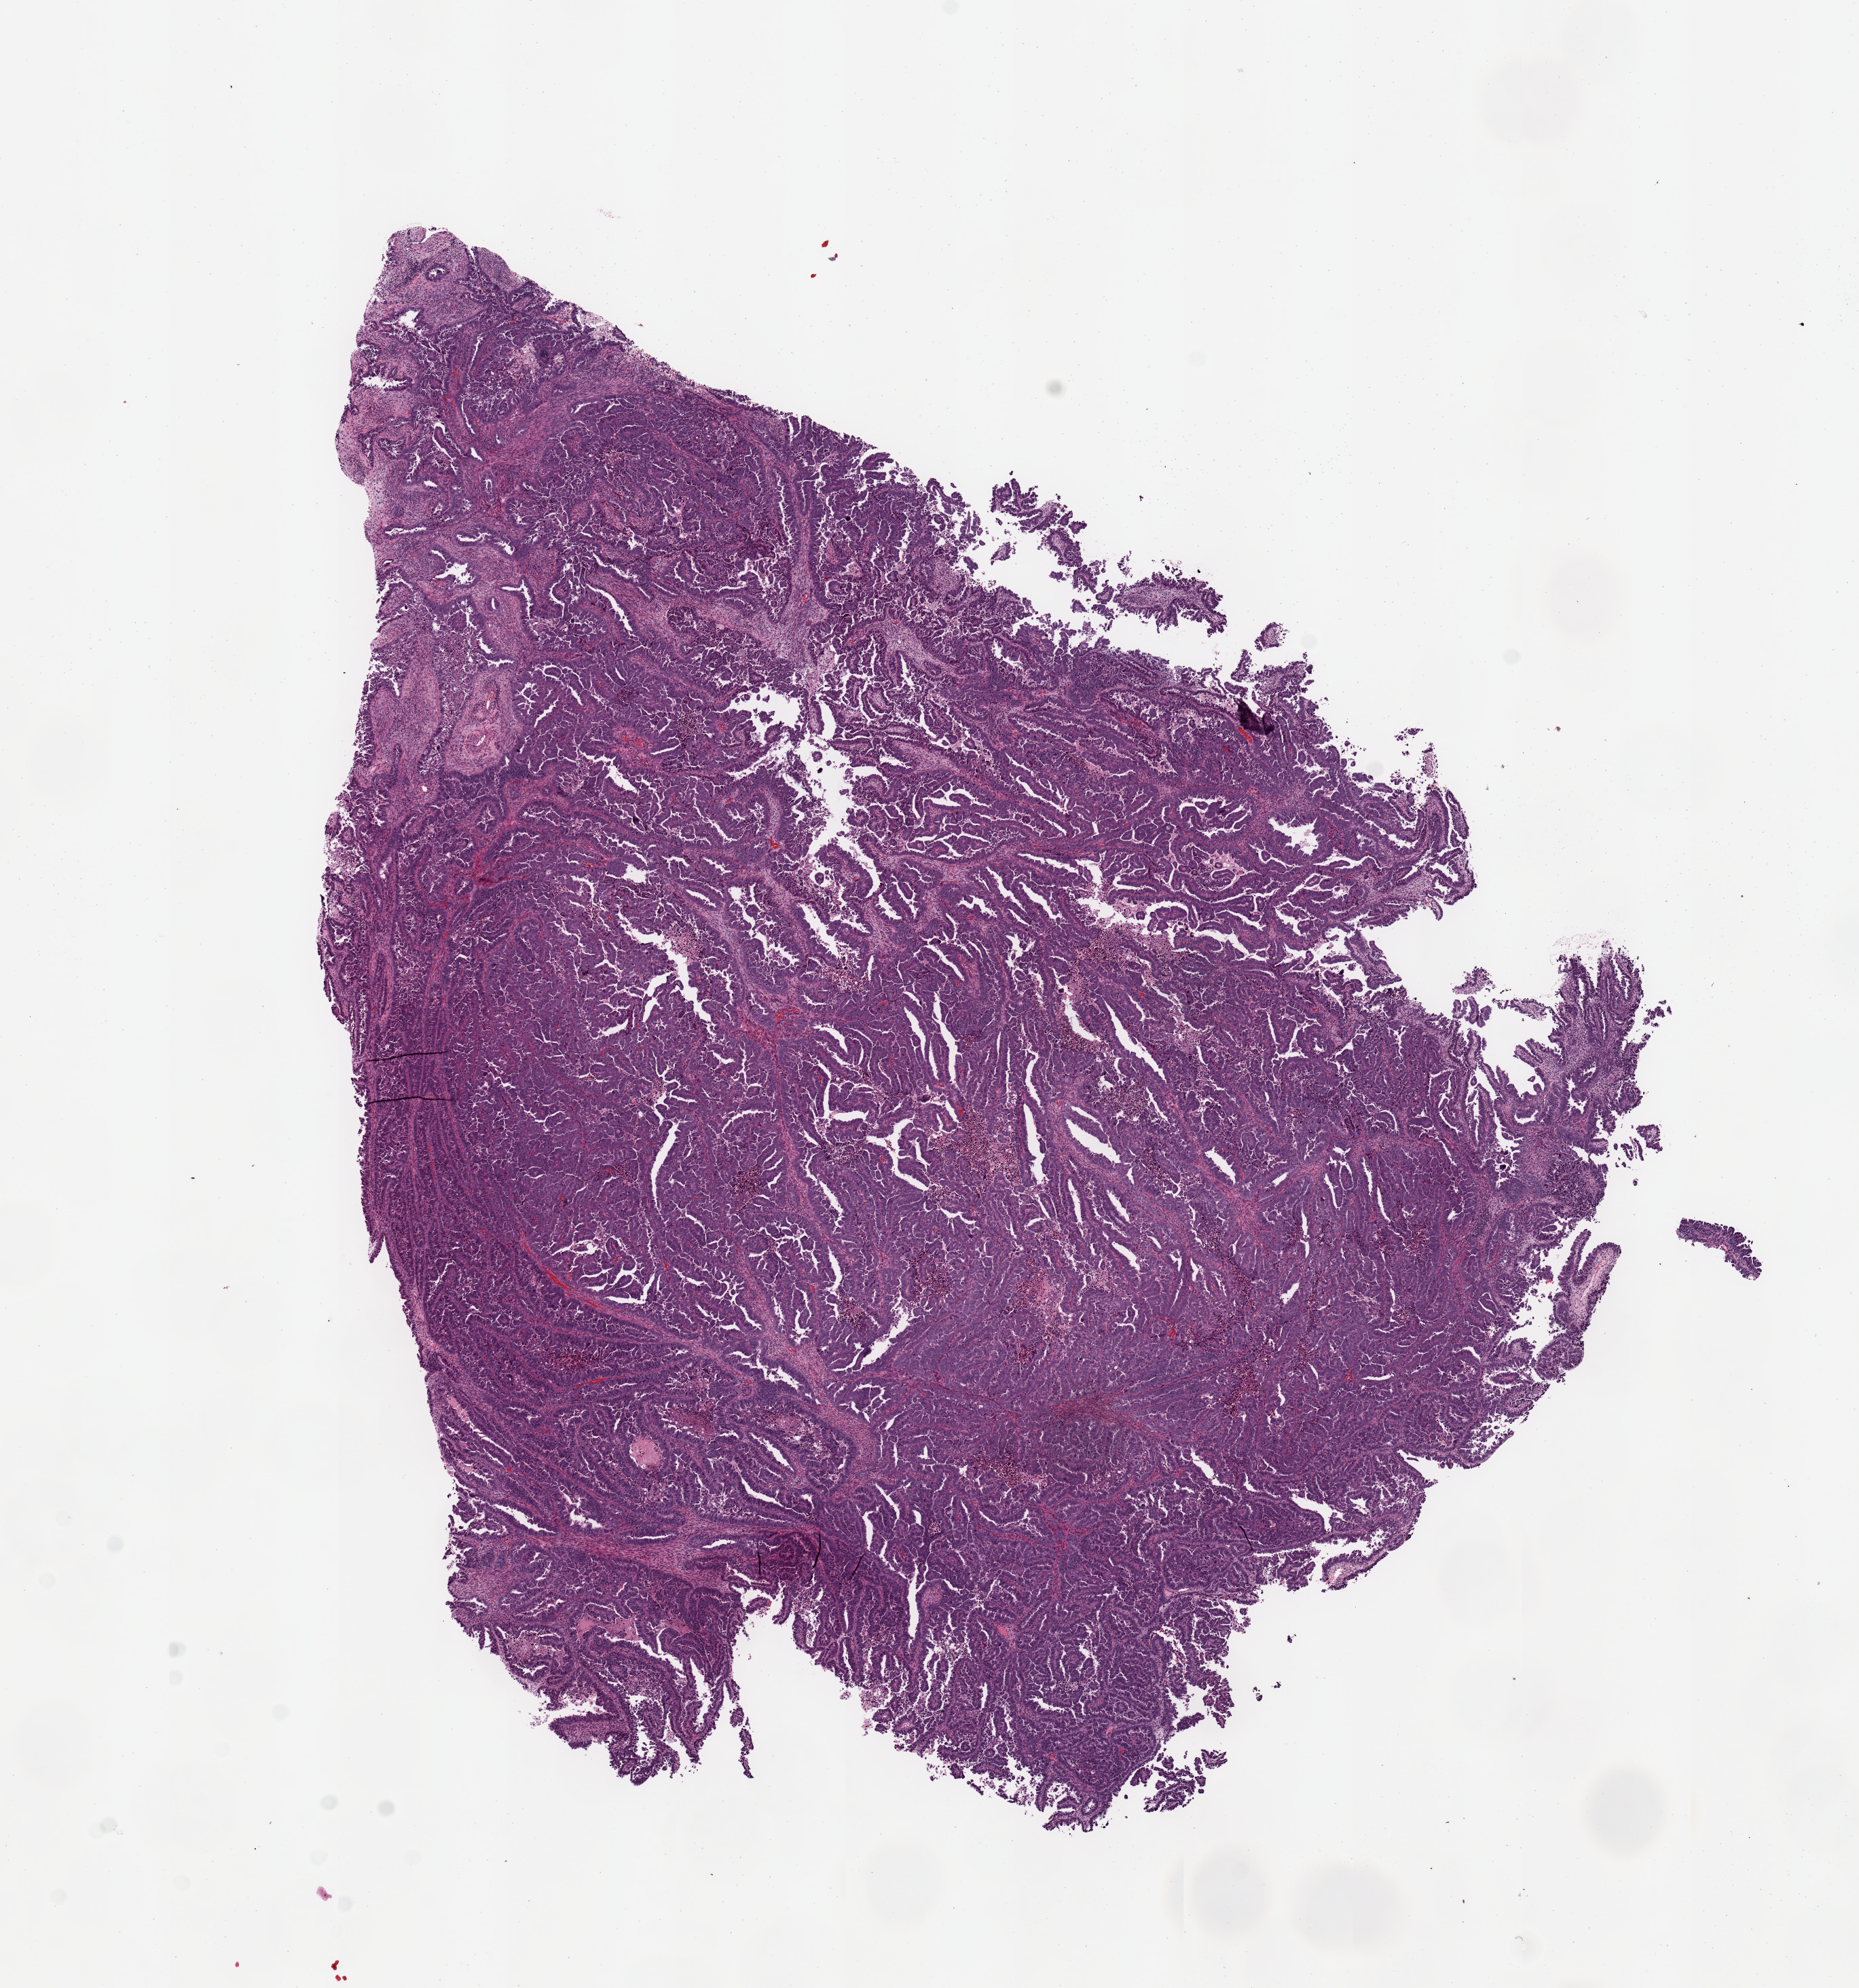
Digitized Hematoxylin and eosin (H&E) stained tissue section (whole slide), low-resolution overview of the scanned area, about 10.8 x 11.6 mm (from a 20x scan), uterus, tumour tissue. 83-year-old female patient.
AJCC pathologic stage: III. Diagnosis: Endometrioid adenocarcinoma, NOS.